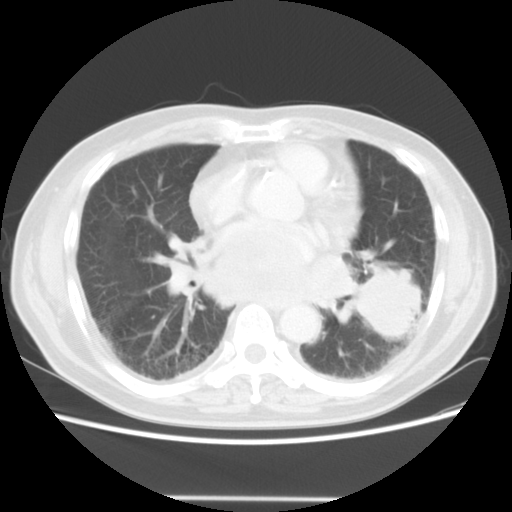
Chest CT, one axial slice; slice 23 of 56 in the series (ordered by position); 140 kVp; lung window (W 1500 / L -600 HU); 512 × 512 image matrix, field of view 360 × 360 mm. Male patient, age 66 years. Case-level facts recorded for this patient, not image findings: clinical TNM (as recorded): T4 N3 M0; histopathological grade: G3.
Annotated regions visible in this slice (bounding box drawn by a radiologist):
- lung tumour (recorded histology: small cell carcinoma): bounding box [x1, y1, x2, y2] px = [352, 258, 430, 343]